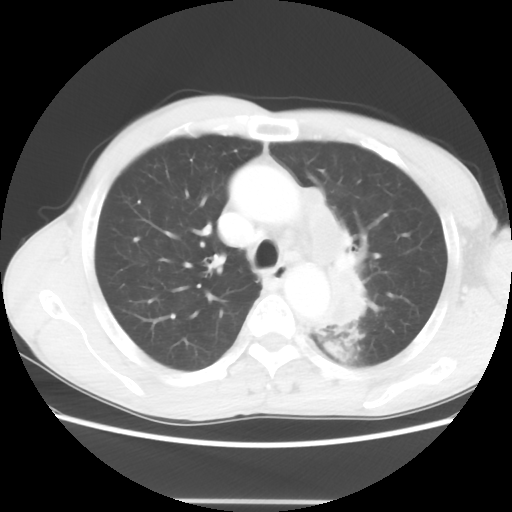
Chest CT, one axial slice. Slice 45 of 62 in the series (ordered by position). 100 kVp. Lung window (W 1500 / L -600 HU). 5 mm slice thickness. 512 × 512 image matrix, field of view 360 × 360 mm. Patient: male, 61 years. From the clinical record (not read from this slice): clinical TNM (as recorded): T3 N1 M1.
Outlined on this slice (rectangle marked by the reading radiologist):
- lung tumour (recorded histology: adenocarcinoma): box from (x=298, y=180) to (x=379, y=333) px